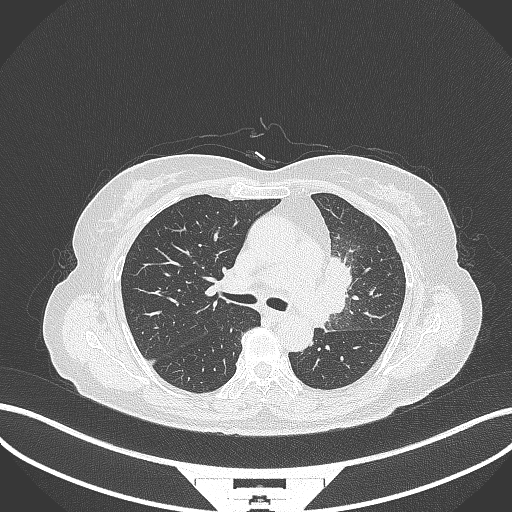
Chest CT, one axial slice; reconstruction kernel B70f; 120 kVp; lung window (W 1500 / L -600 HU); 1 mm slice thickness; 512 × 512 image matrix. Female patient, age 64 years. From the clinical record (not read from this slice): clinical TNM (as recorded): T2a N2 M0.
Outlined on this slice (bounding box drawn by a radiologist):
- lung tumour (recorded histology: adenocarcinoma): box from (x=317, y=252) to (x=355, y=319) px